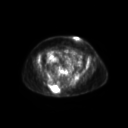
FDG PET of an extremity soft-tissue mass (from a PET/CT study), one axial slice. Position 77 of 267 along the scan axis. 3.27 mm slice thickness. 128 × 128 image matrix, field of view 600 × 600 mm. Female patient, age 60 years. Case-level facts recorded for this patient, not image findings: histological type: spindle cell suggestive of myxofibrosarcoma; grade: intermediate; site of the primary tumour: right buttock.
Structures marked on this image (expert contour drawn on MRI and transferred to this co-registered scan by the dataset authors):
- gross tumour volume (mass): bounding box <47,83,62,94> (left, top, right, bottom; pixels)